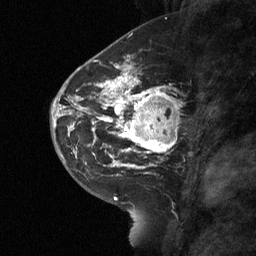
Breast MRI (dynamic contrast-enhanced), one sagittal slice; slice 28 of 64 in the series (ordered by position); dynamic contrast-enhanced study with each time point stored as its own series, time point 2 of 3 at this slice position (early post-contrast, ordered by acquisition time); 1.5 T; TE 4.8 ms, TR 27 ms; 2 mm slice thickness; 256 × 256 image matrix. Female patient, age 42 years. Case-level facts recorded for this patient, not image findings: setting: breast cancer imaged before/during neoadjuvant chemotherapy; receptor status: triple-negative.
Structures marked on this image (semi-automatically segmented with operator editing):
- analysis volume of interest (the breast-tissue region the enhancement analysis was run in; not a lesion): bounding box <115,85,178,160> (left, top, right, bottom; pixels)
- tumour enhancement mask (voxels above the 90 % enhancement threshold inside the analysis volume of interest): <115,85,170,155>